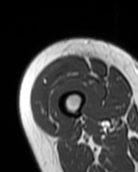
MRI of an extremity soft-tissue mass, one axial slice; position 17 of 99 along the scan axis; MR volume resampled by the dataset authors to the PET/CT grid (not the native acquisition matrix); 3.27 mm slice thickness; 138 × 172 image matrix, field of view 135 × 168 mm. Female patient. From the clinical record (not read from this slice): histological type: pleiomorphic undifferentiated sarcoma; grade: high; site of the primary tumour: right quadricep.
Structures marked on this image (expert contour drawn on MRI and transferred to this co-registered scan by the dataset authors):
- gross tumour volume including surrounding oedema: bounding box [x1, y1, x2, y2] px = [32, 57, 88, 119]